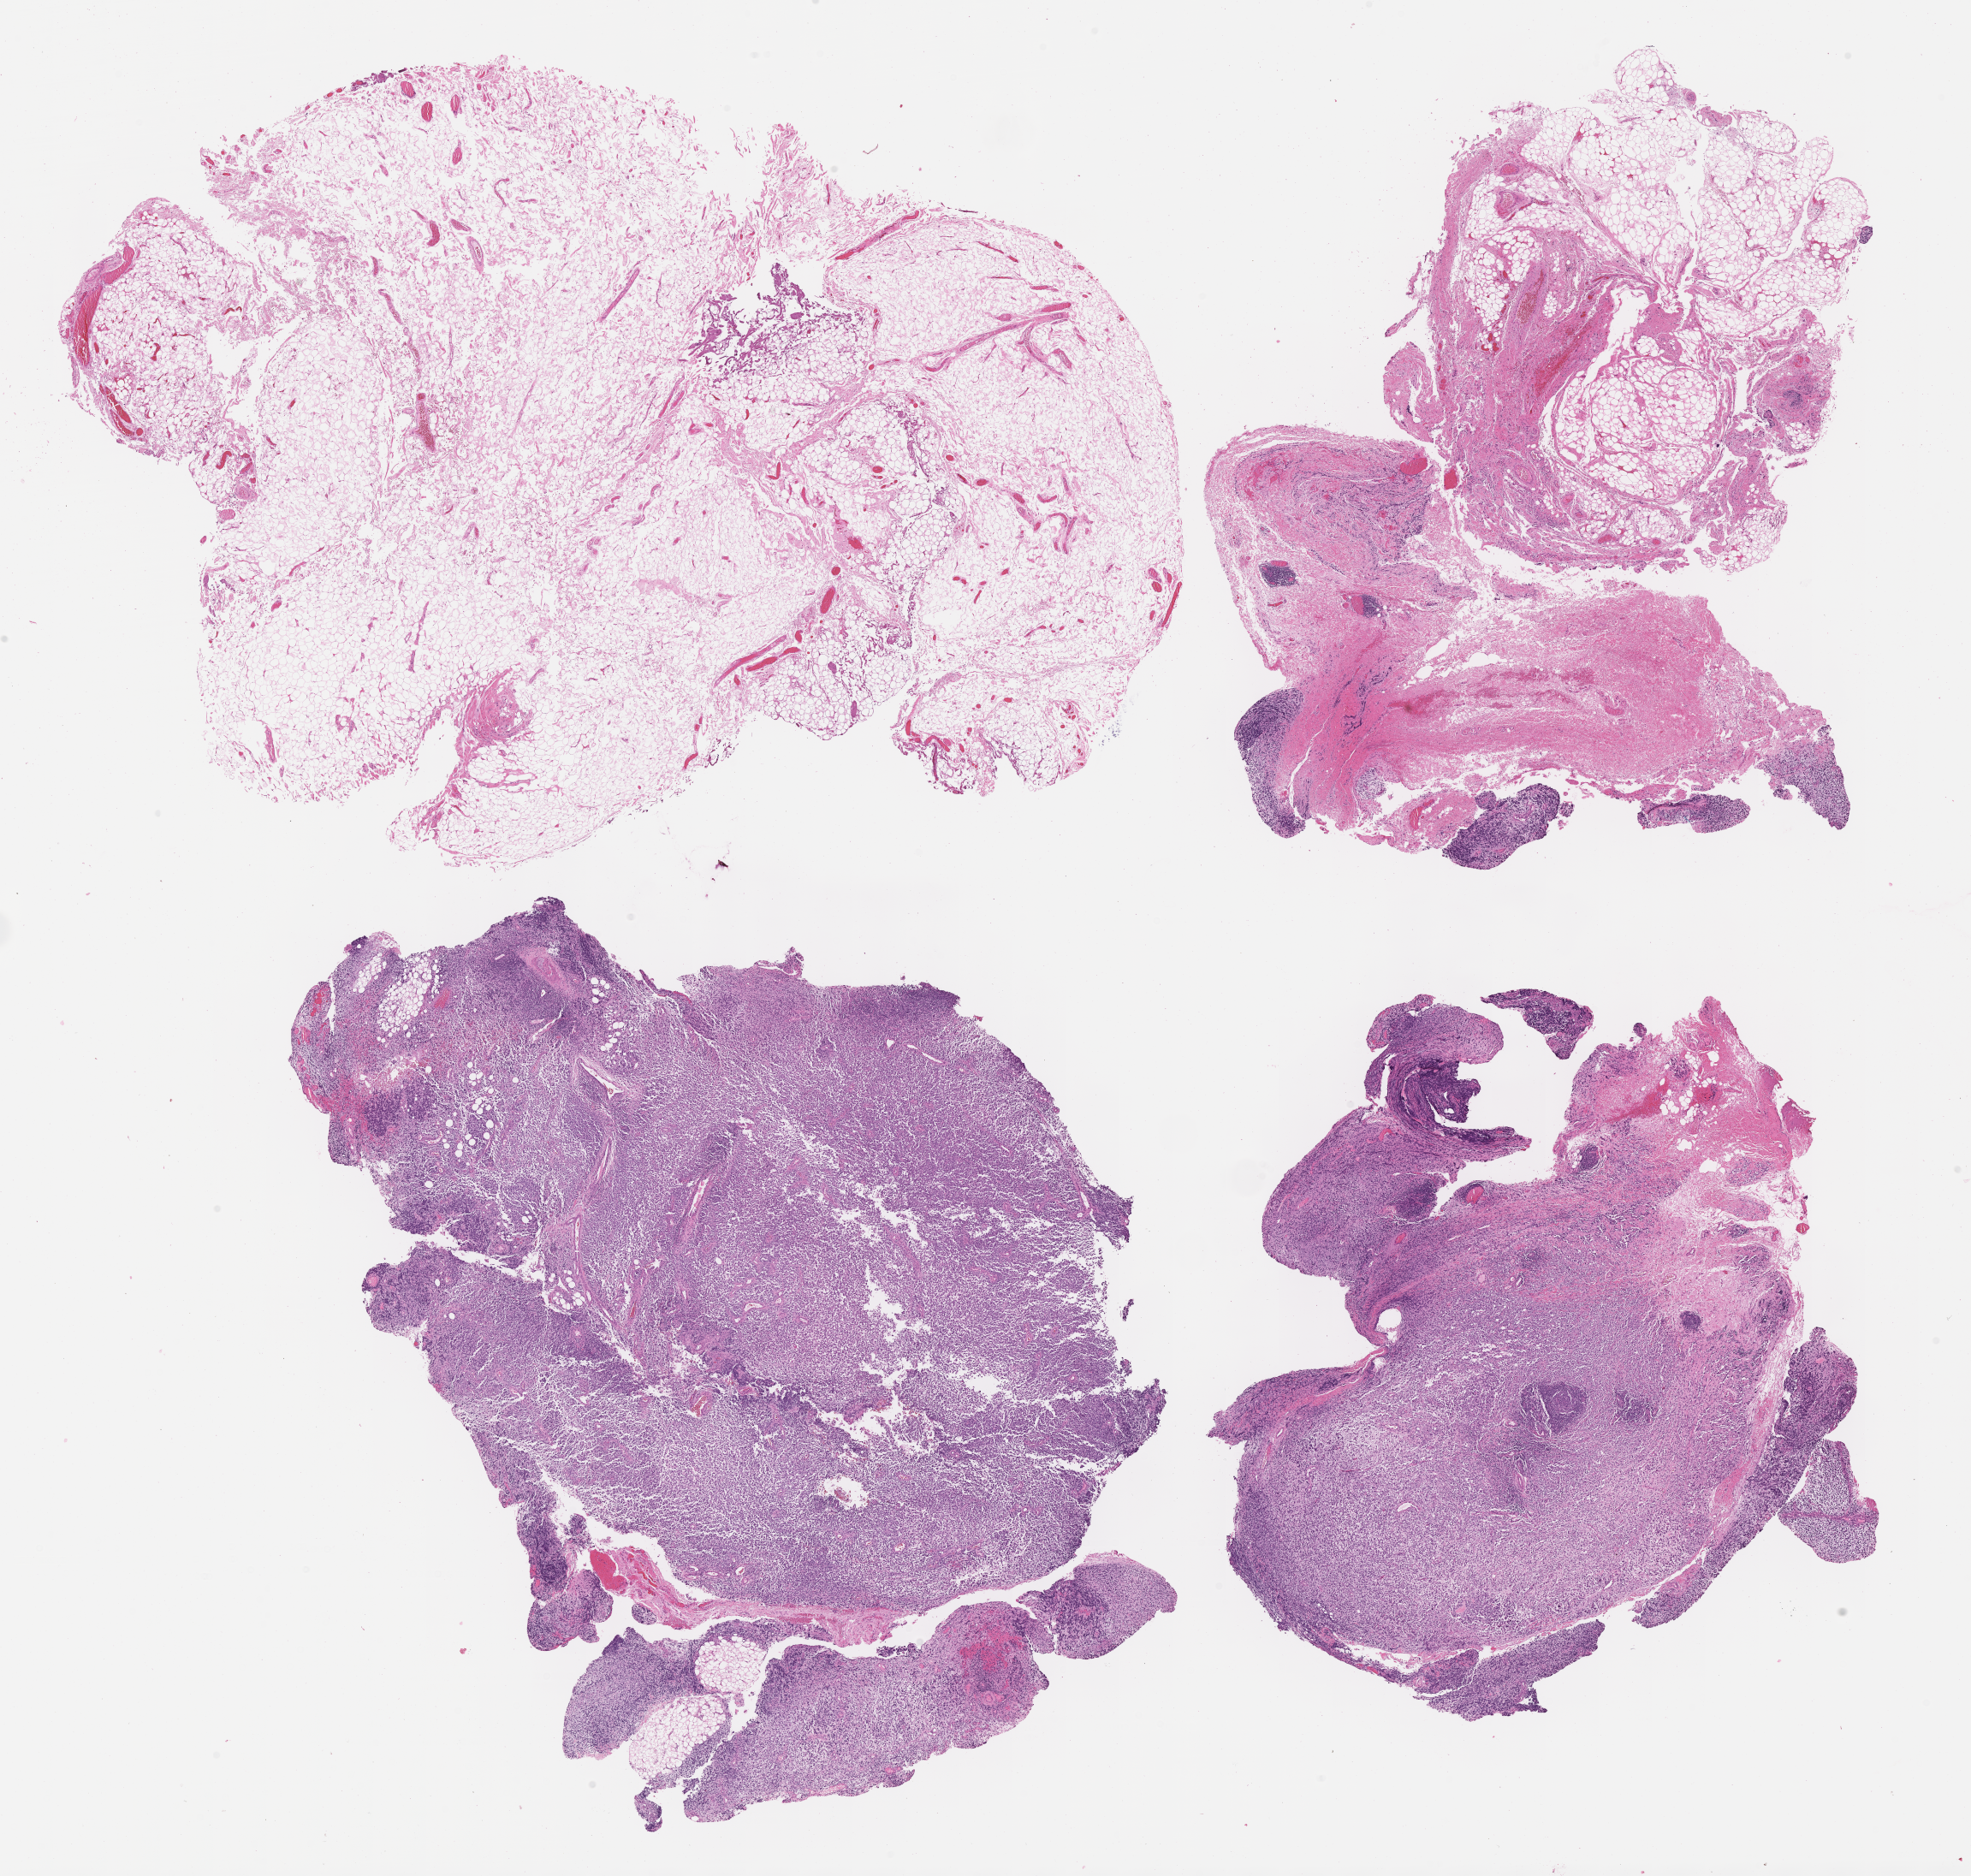
Haematoxylin and eosin whole-slide image of tumor tissue — a low-resolution overview of the entire scanned area, about 18.6 x 17.7 mm. FFPE section. Patient: male, age 6.0 years at diagnosis.
Diagnosis: rhabdomyosarcoma; histological classification: embryonal rhabdomyosarcoma. Stage (as recorded): 1.